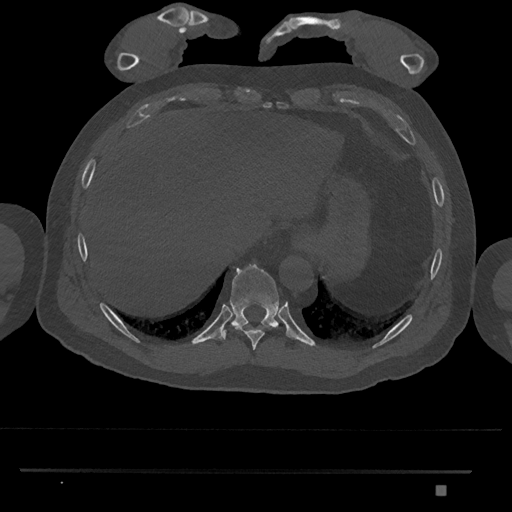
CT including the spine, one axial slice. Position 1026 of 1134 along the scan axis. Reconstruction kernel Br40s/3. 120 kVp. Bone window (W 1800 / L 400 HU). 512 × 512 image matrix, field of view 429 × 429 mm. Patient: male, 65 years. From the clinical record (not read from this slice): primary cancer: prostate.
Outlined on this slice (semi-automatically segmented with operator editing):
- T10 vertebra: bounding box [x1, y1, x2, y2] px = [220, 264, 279, 340]
- T9 vertebra: [233, 325, 277, 350]